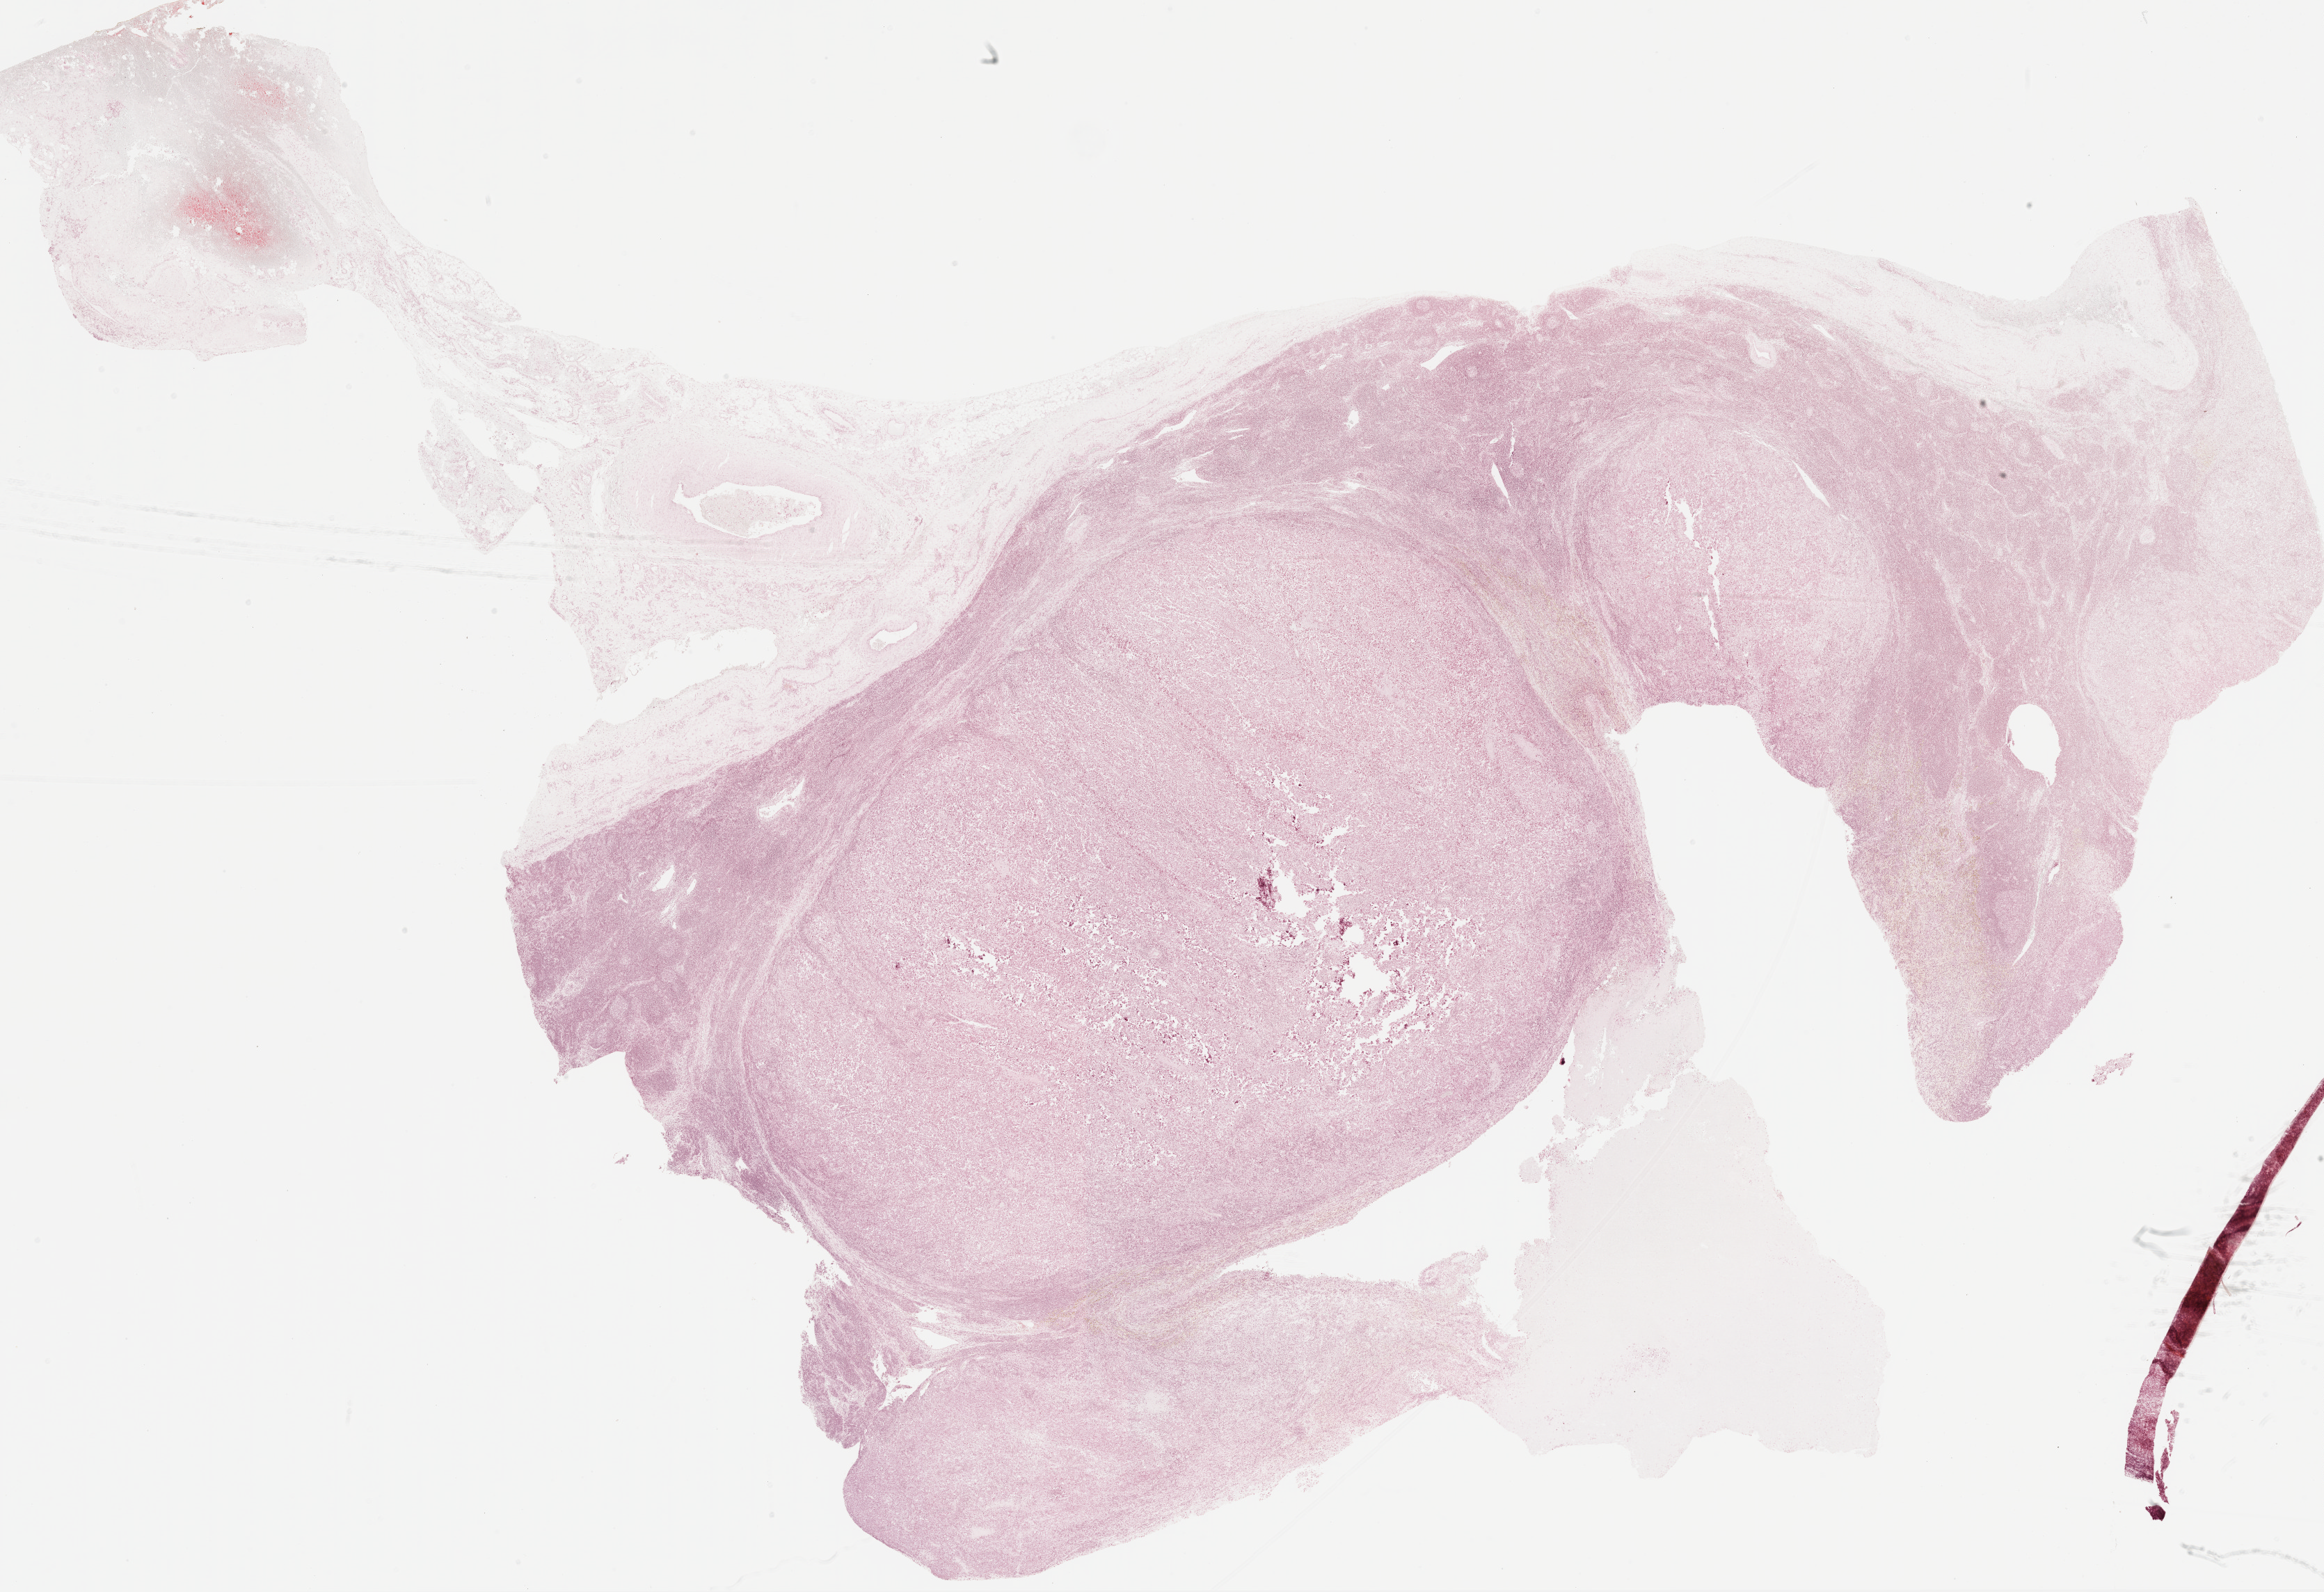
H&E-stained whole-slide image — whole scanned area (about 26.9 x 18.5 mm) shown as a low-resolution overview, FFPE section, metastatic tumour sample, sampled site not recorded. Female patient; age at initial diagnosis 50 years.
This section: metastatic tumour tissue. Patient diagnosis: Malignant melanoma, NOS.